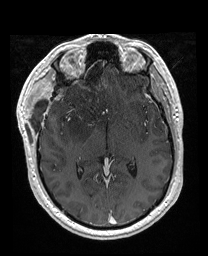
Brain MRI from a brain-tumour surgery series, one axial slice; slice 101 of 176 in the series (ordered by position); T1-weighted post-contrast; 1 mm slice thickness; 208 × 256 image matrix, field of view 208 × 256 mm. Case-level facts recorded for this patient, not image findings: histopathology: Astrocytoma; WHO grade: 4; IDH mutation: yes; tumour location: Right Orbitofrontal Anterior Temporal Insular.
Structures marked on this image (outlined manually by an expert reader):
- previous resection cavity: bounding box <61,55,83,83> (left, top, right, bottom; pixels)